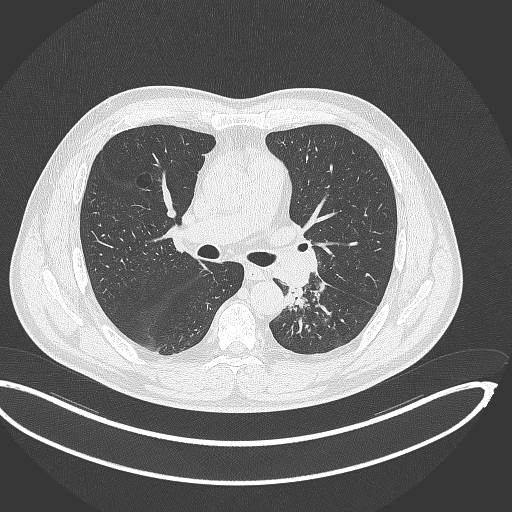
Chest CT, one axial slice. Position 210 of 362 along the scan axis. Reconstruction kernel B70f. 120 kVp. Lung window (W 1500 / L -600 HU). 512 × 512 image matrix, field of view 442 × 442 mm. Patient: male, 50 years. From the clinical record (not read from this slice): clinical TNM (as recorded): T2a N3 M0.
Annotated regions visible in this slice (rectangle marked by the reading radiologist):
- lung tumour (recorded histology: squamous cell carcinoma): bounding box (x1, y1, x2, y2) in pixels: (282, 285, 309, 312)